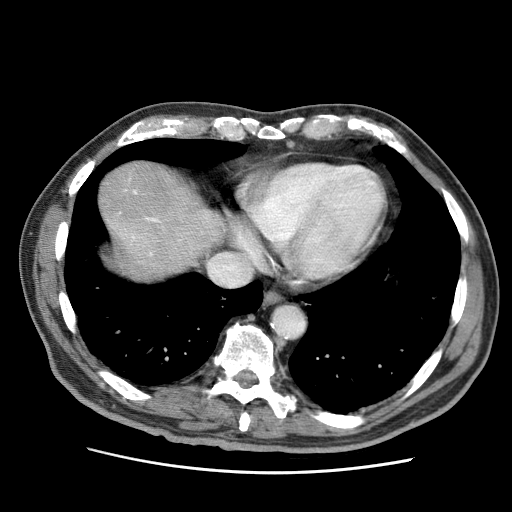
Contrast-enhanced abdominal CT (liver protocol), one axial slice; position 62 of 75 along the scan axis; reconstruction kernel STANDARD; 120 kVp; soft-tissue window (W 400 / L 40 HU); 2.5 mm slice thickness; 512 × 512 image matrix. From the clinical record (not read from this slice): diagnosis: hepatocellular carcinoma (patient treated with transarterial chemoembolisation; whether this scan precedes or follows treatment is not stated here); TNM stage (as recorded): Stage-IIIA; Child-Pugh class: A; tumour differentiation: well differentiated.
Annotated regions visible in this slice (semi-automatically segmented with operator editing):
- liver parenchyma outside the tumour (the mass and vessels are separate outlines, so this box may not span the whole liver): bounding box <99,162,222,280> (left, top, right, bottom; pixels)
- liver vessels: <131,190,181,256>